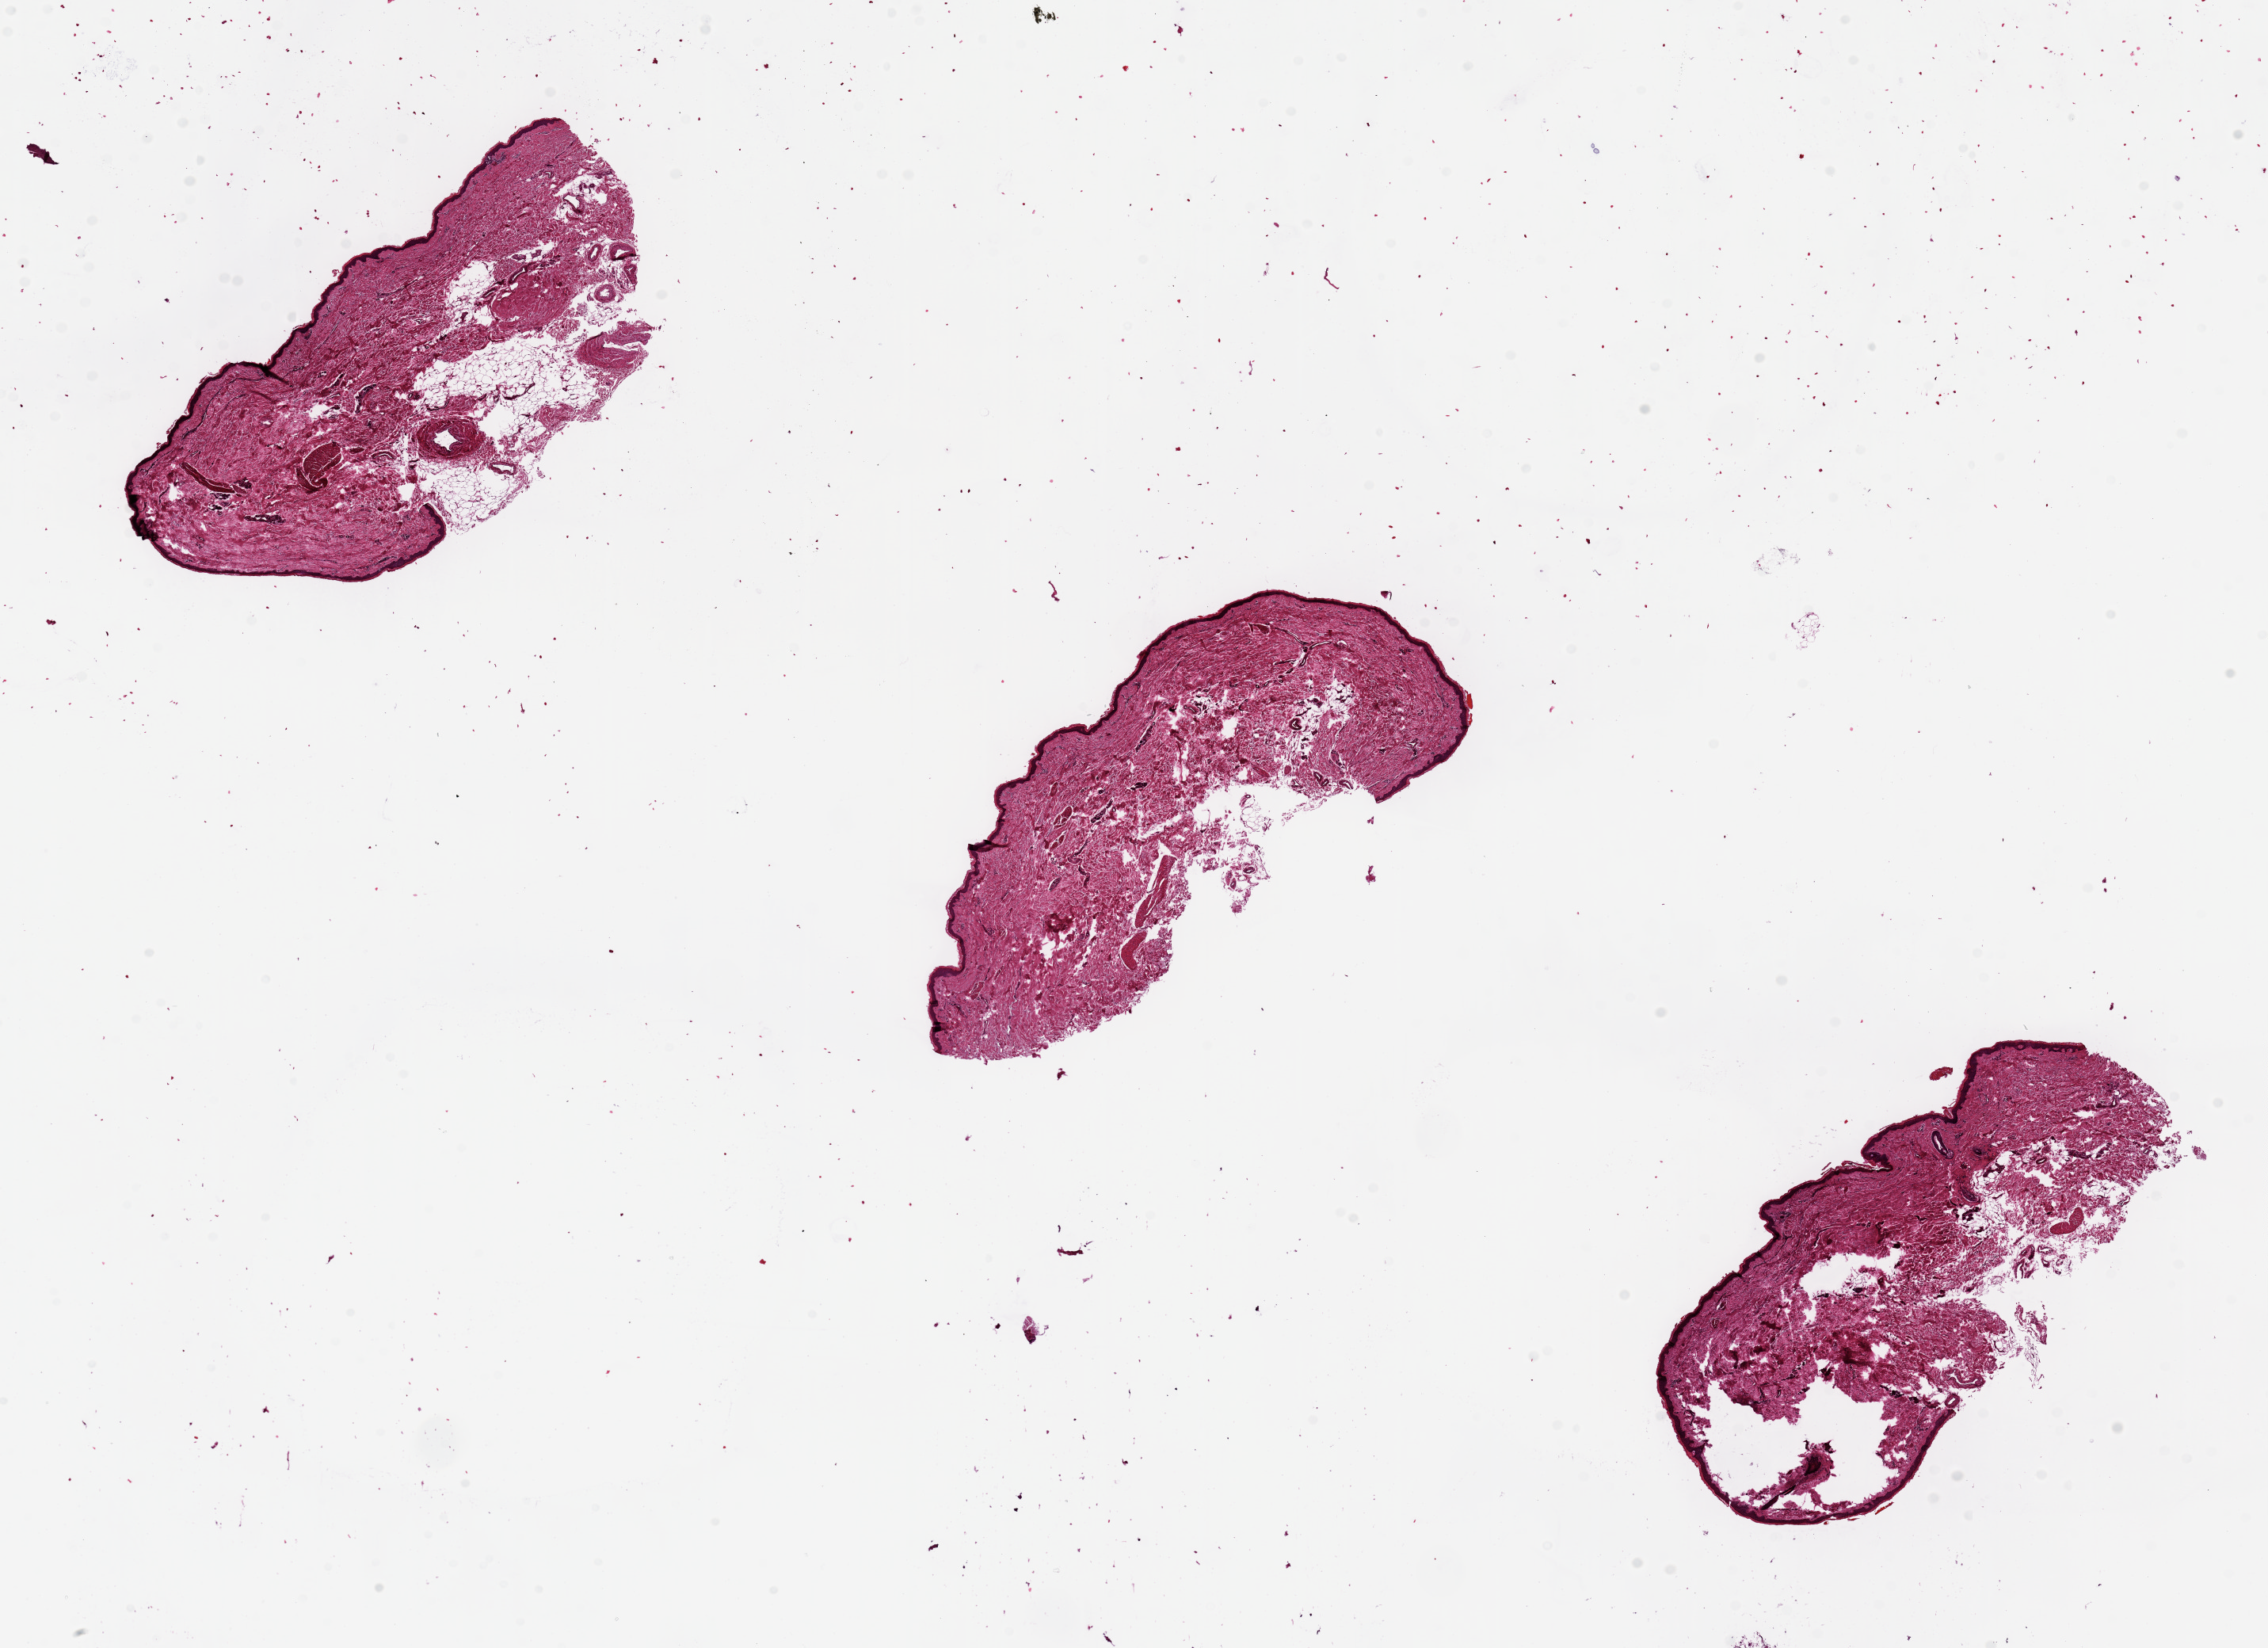
Whole-slide image, haematoxylin and eosin stain — shown as a low-resolution overview of the whole scanned area (about 22.6 x 16.4 mm); PAXgene-fixed, paraffin-embedded tissue; section of skin of lower leg (target tissue); tissue donor sample.
Review note (as recorded): 3 pieces.